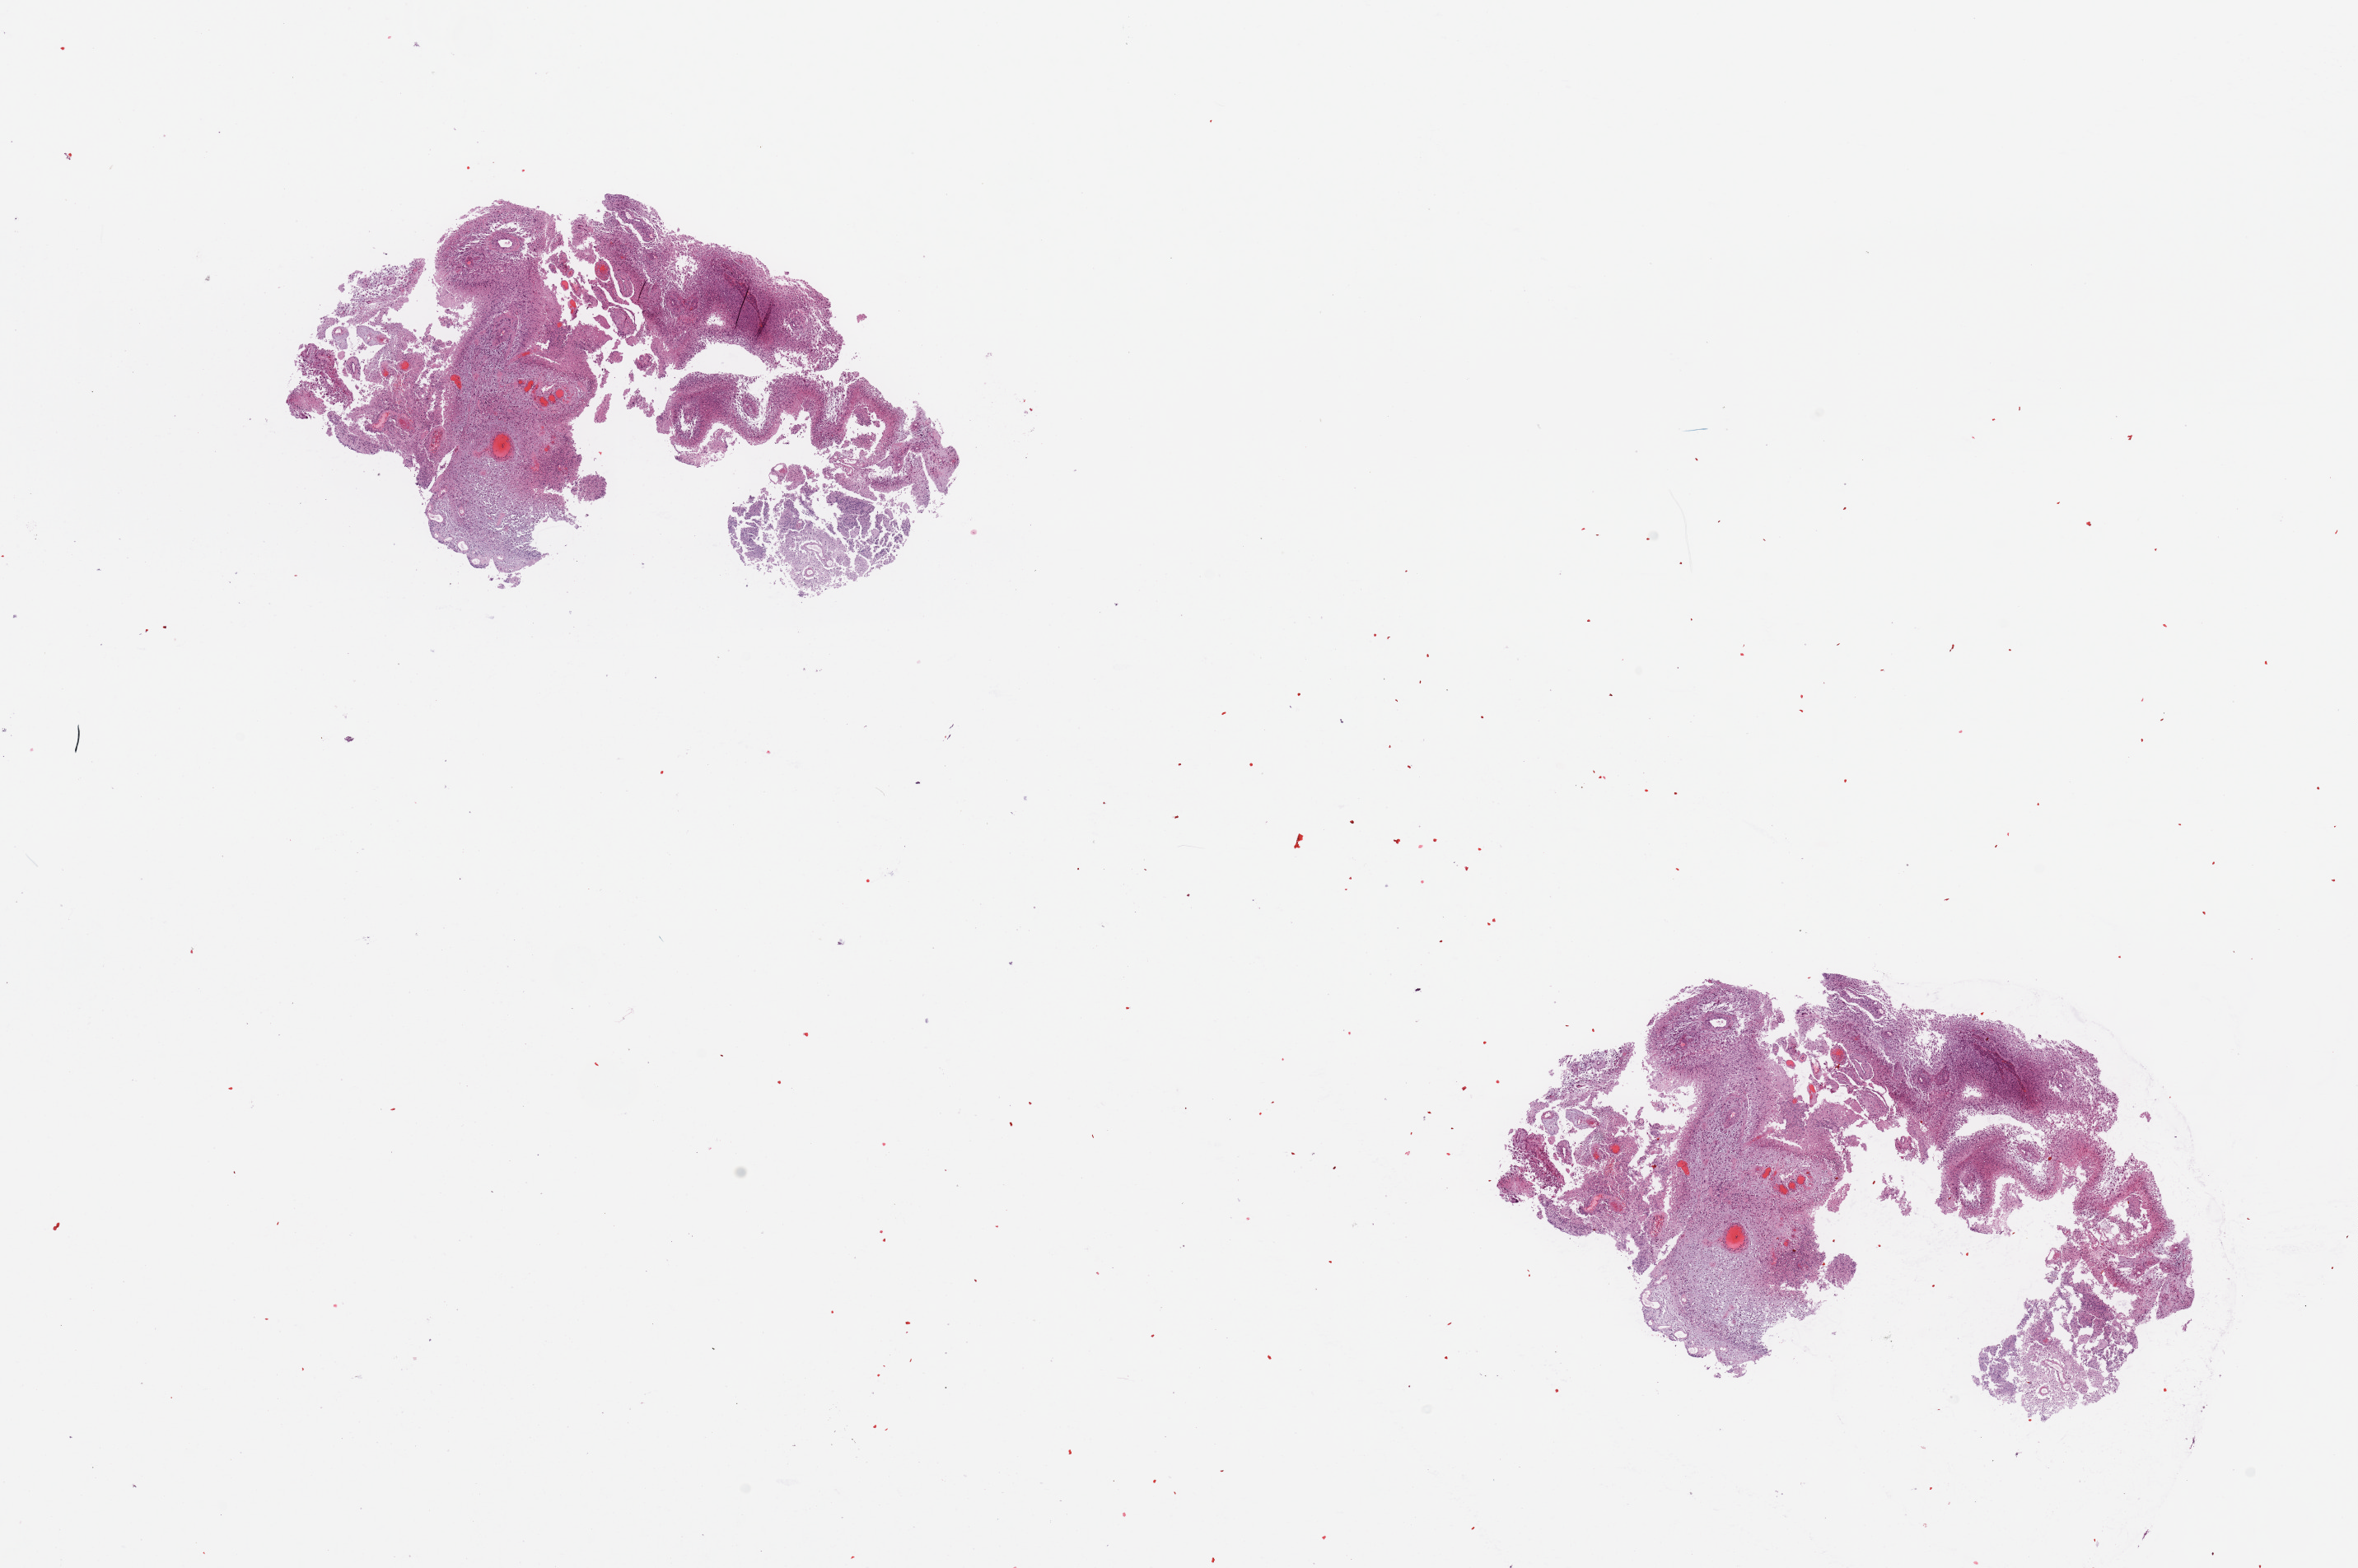
Digitized Hematoxylin and eosin (H&E) stained tissue section (whole slide) — whole scanned area (about 22.6 x 15.1 mm) shown as a low-resolution overview; tumour tissue sample, sampled site: brain. Male, 37 y/o. Composition of this section per pathologist review: tumour nuclei 70%, necrosis 20%.
Diagnosis: Glioblastoma.